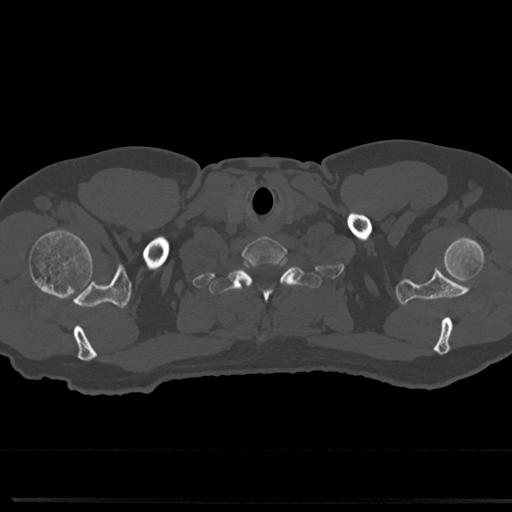
CT including the spine, one axial slice. Position 686 of 817 along the scan axis. Reconstruction kernel Br40s/3. 120 kVp. Bone window (W 1800 / L 400 HU). 0.5 mm slice thickness. 512 × 512 image matrix. Male patient, age 61 years. Case-level facts recorded for this patient, not image findings: primary cancer: prostate.
Outlined on this slice (semi-automatically segmented with operator editing):
- T1 vertebra: box from (x=215, y=260) to (x=316, y=345) px